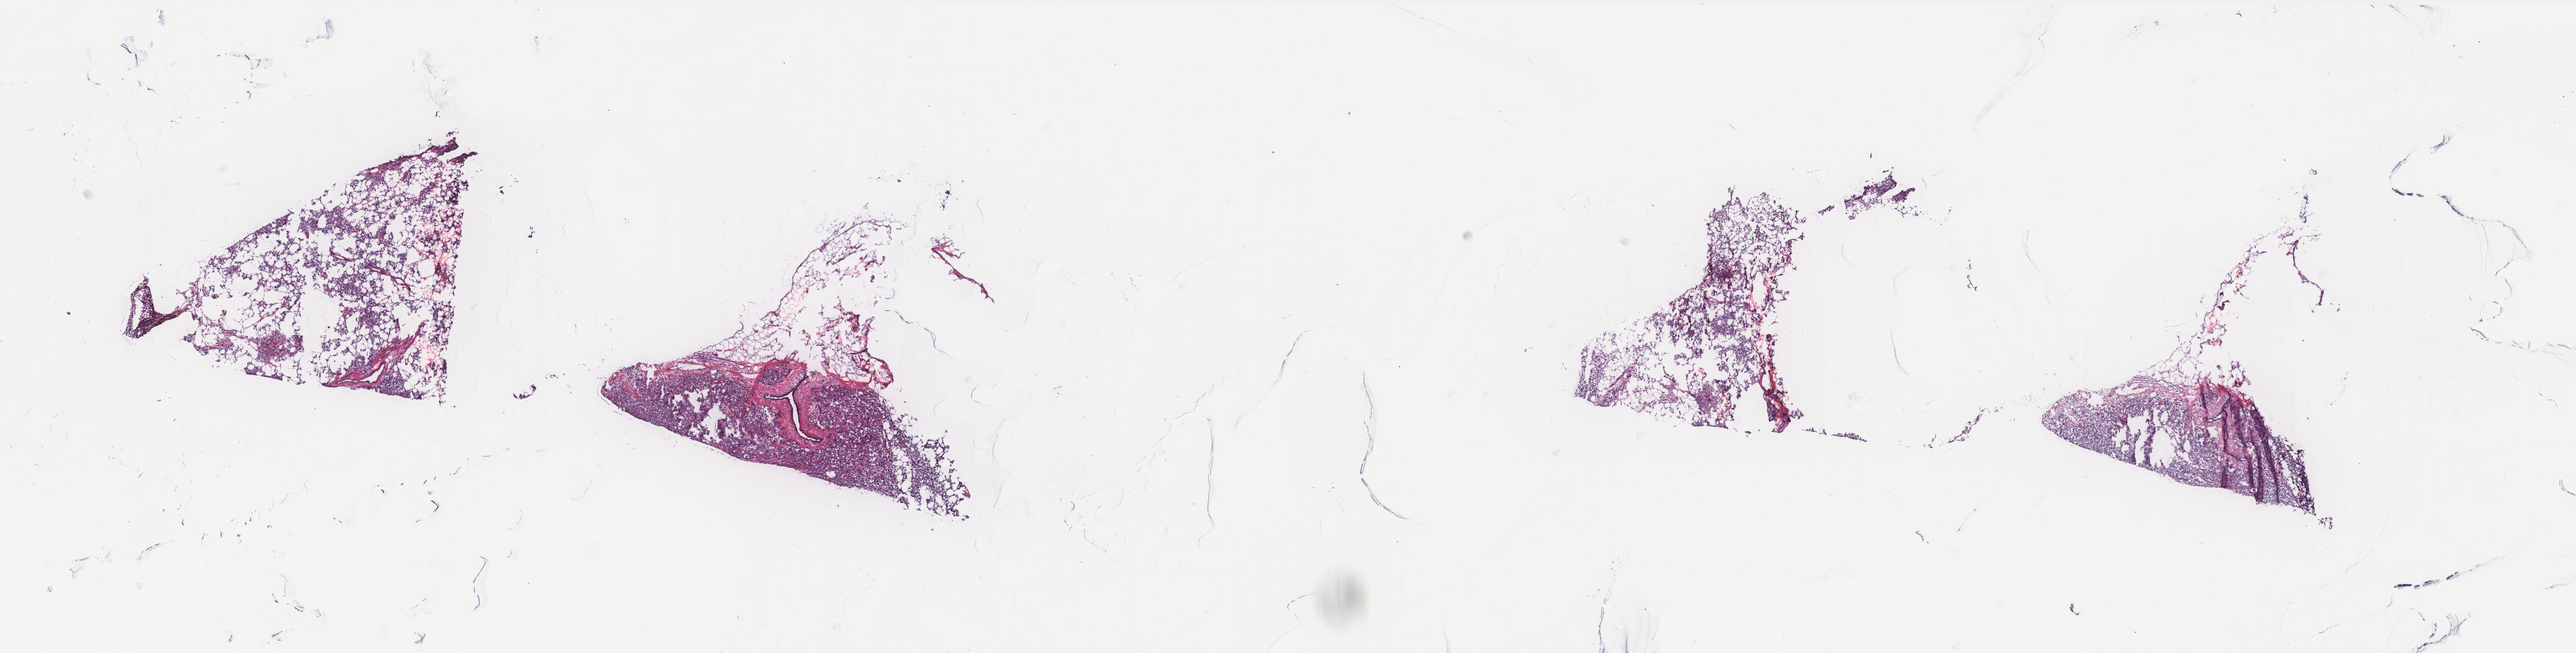
H&E-stained whole-slide image — shown as a low-resolution overview of the whole scanned area (about 30.1 x 7.6 mm, acquisition: 40x scan); frozen section from the bottom of the tissue portion; sample: primary tumour, breast. Female patient; age at initial diagnosis 51 years. Composition of this section per pathologist review: tumour cells 80%, tumour nuclei 80%, normal cells 0%, stromal cells 20%, necrosis 0%. Infiltration values recorded for this section: lymphocyte infiltration 0%, monocyte infiltration 0%, neutrophil infiltration 0%.
- AJCC pathologic stage: IIB
- pathologic diagnosis: Lobular carcinoma, NOS